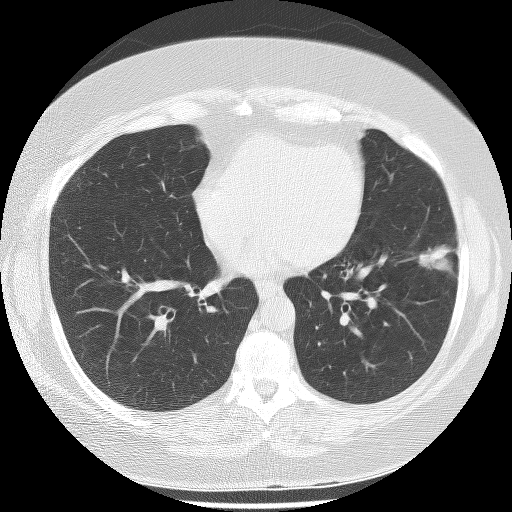
Low-dose screening chest CT, axial slice. Baseline screening round. Lung window (W 1500 / L -600 HU). Lung (sharp) reconstruction kernel (BONE). Slice 127 of 233 in the series. 512 × 512 image matrix. Female, age 56 years at enrolment.
Expert reader's lesion annotation, box from (x=400, y=231) to (x=463, y=281) px. The exam's reader record, not a measurement of the box and not confirmed to be the same lesion: non-calcified nodule or mass ≥4 mm, left lower lobe, 22 × 17 mm, spiculated (stellate) margins, soft tissue attenuation. Official screen result: positive, change unspecified: nodule(s) >= 4 mm or enlarging nodule(s), mass(es), or other non-specific abnormalities suspicious for lung cancer. Participant outcome: lung cancer diagnosed 63 days after this screen — bronchiolo-alveolar adenocarcinoma, NOS, left lower lobe, stage IA (AJCC 6th edition), 18 mm at pathology.